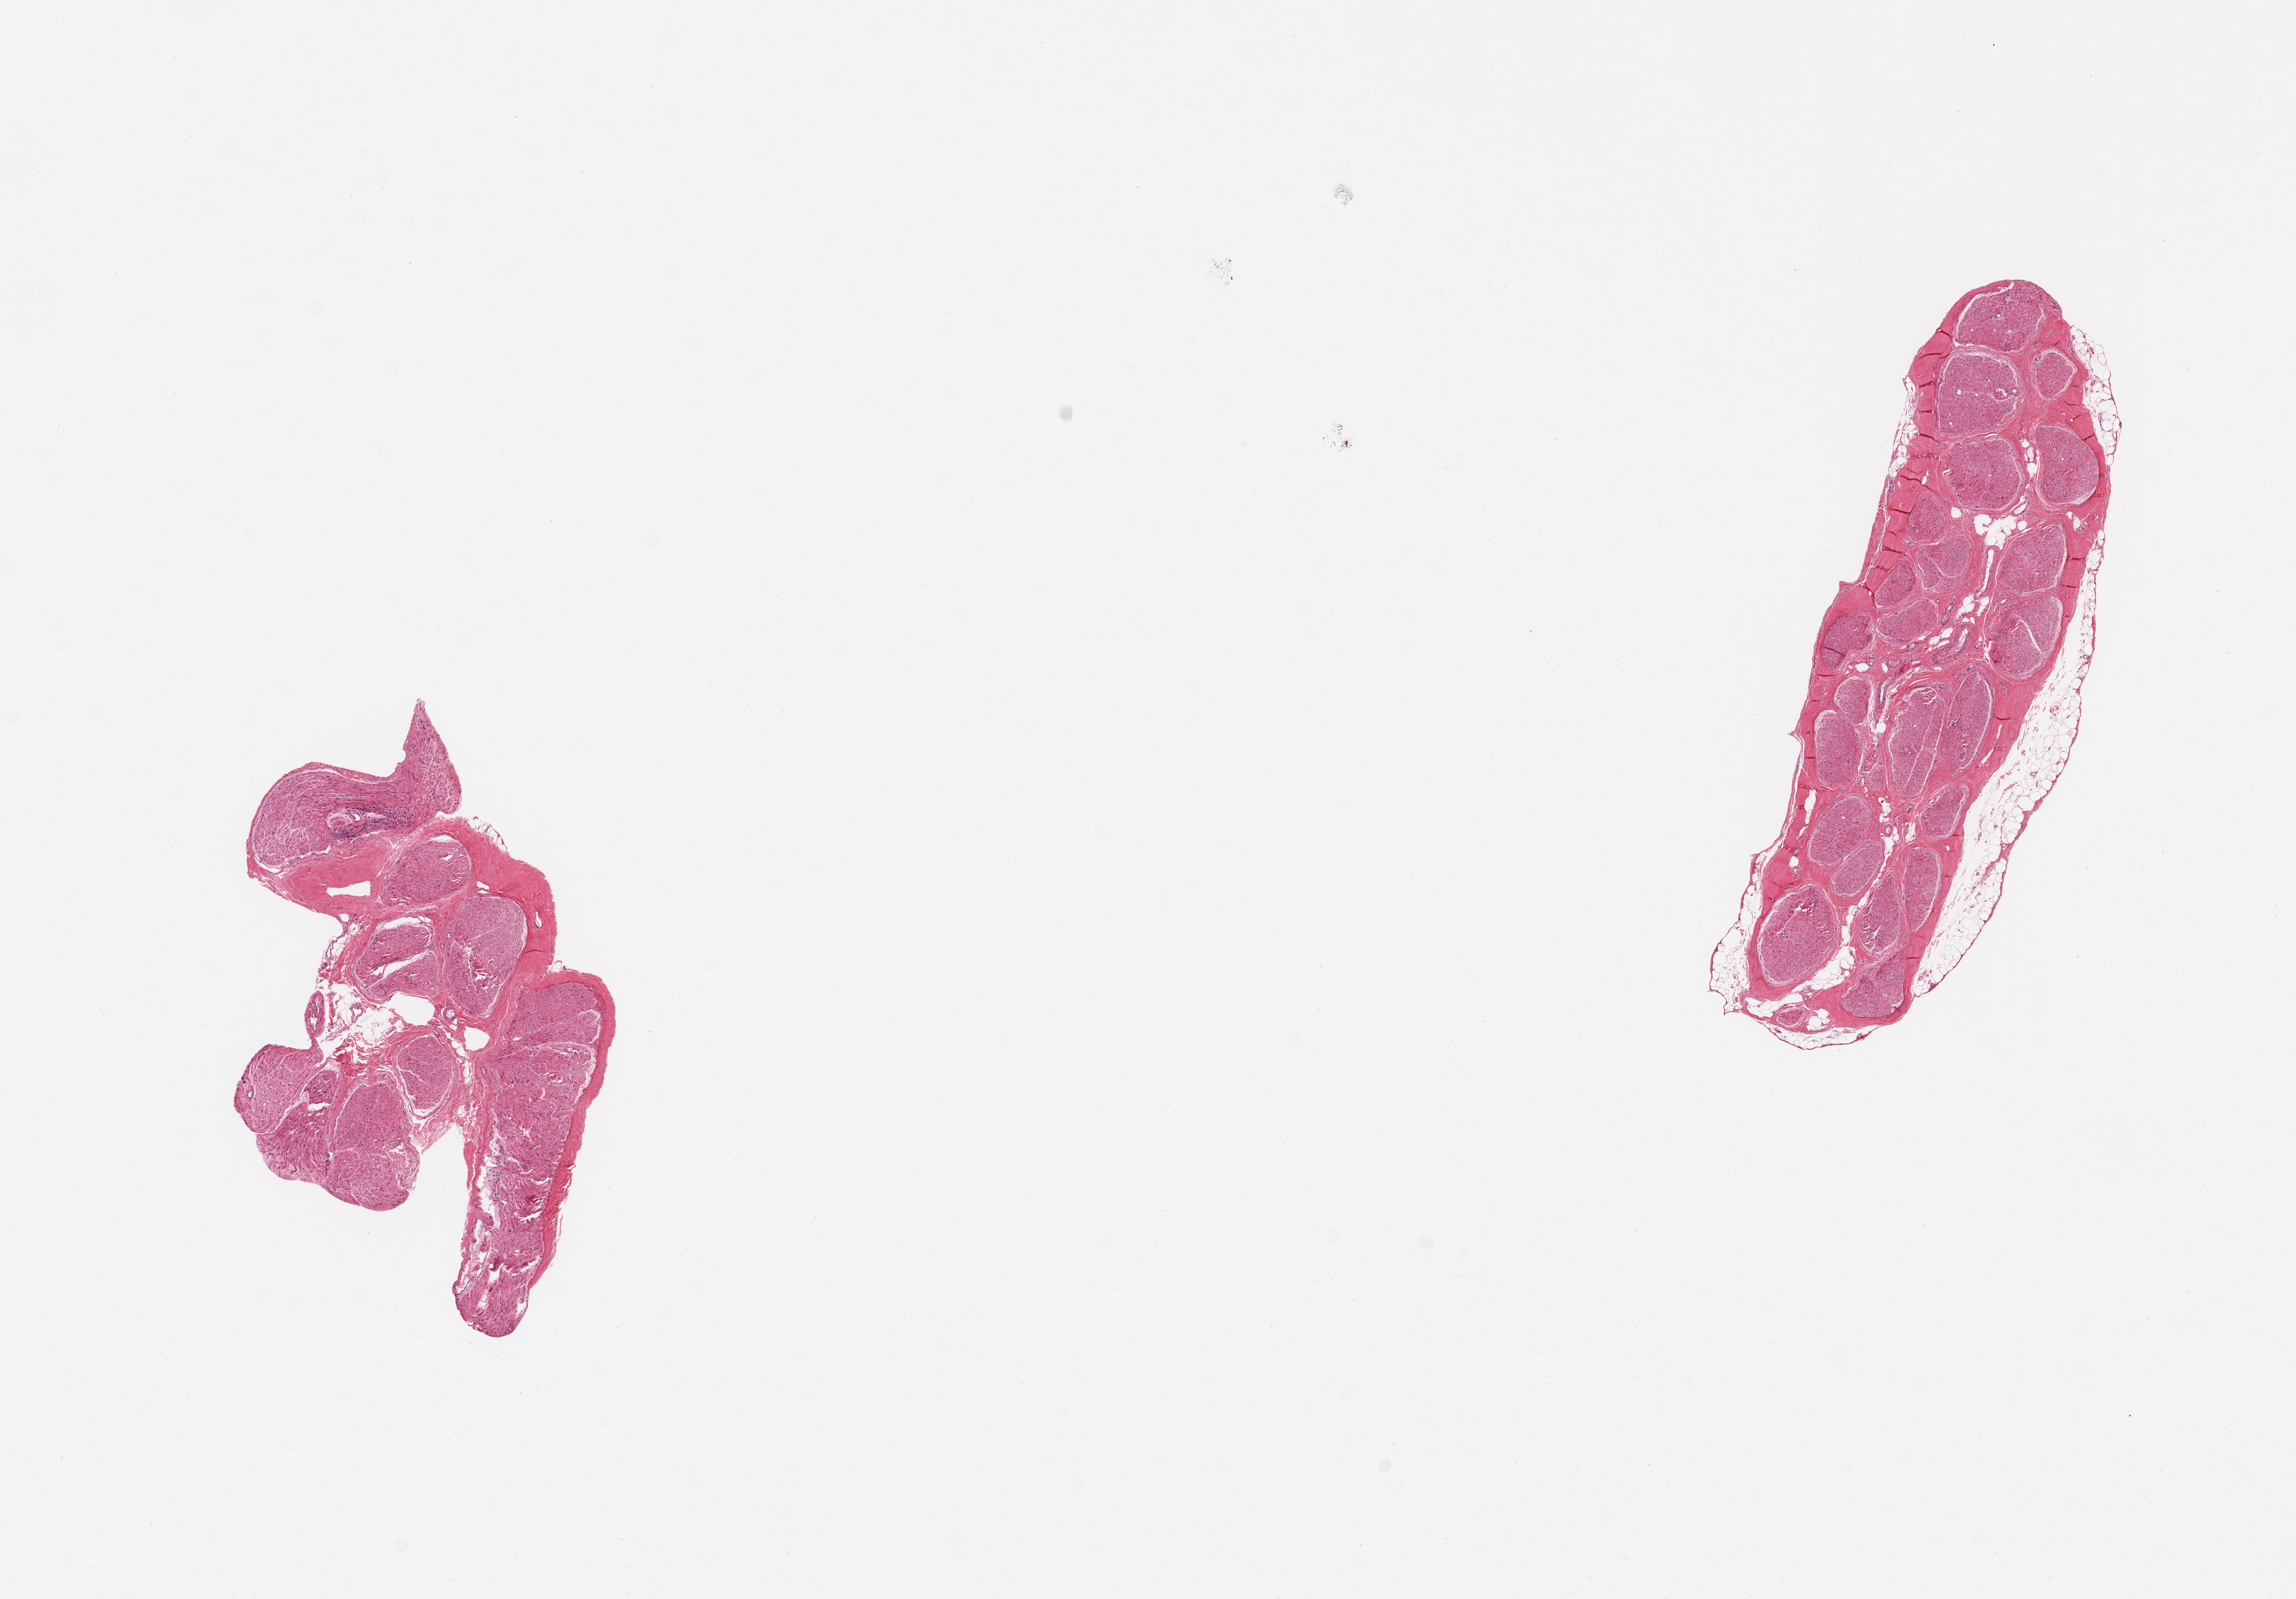
Digitized haematoxylin and eosin-stained section, low-resolution overview of the scanned area, about 14.8 x 10.3 mm (acquisition: 20x scan). PAXgene-fixed paraffin-embedded (PFPE) section. Sampled site (target tissue): tibial nerve. Tissue donor sample. Donor: female.
Review note (as recorded): 2 pieces; 1 piece includes ~10% attached fat.